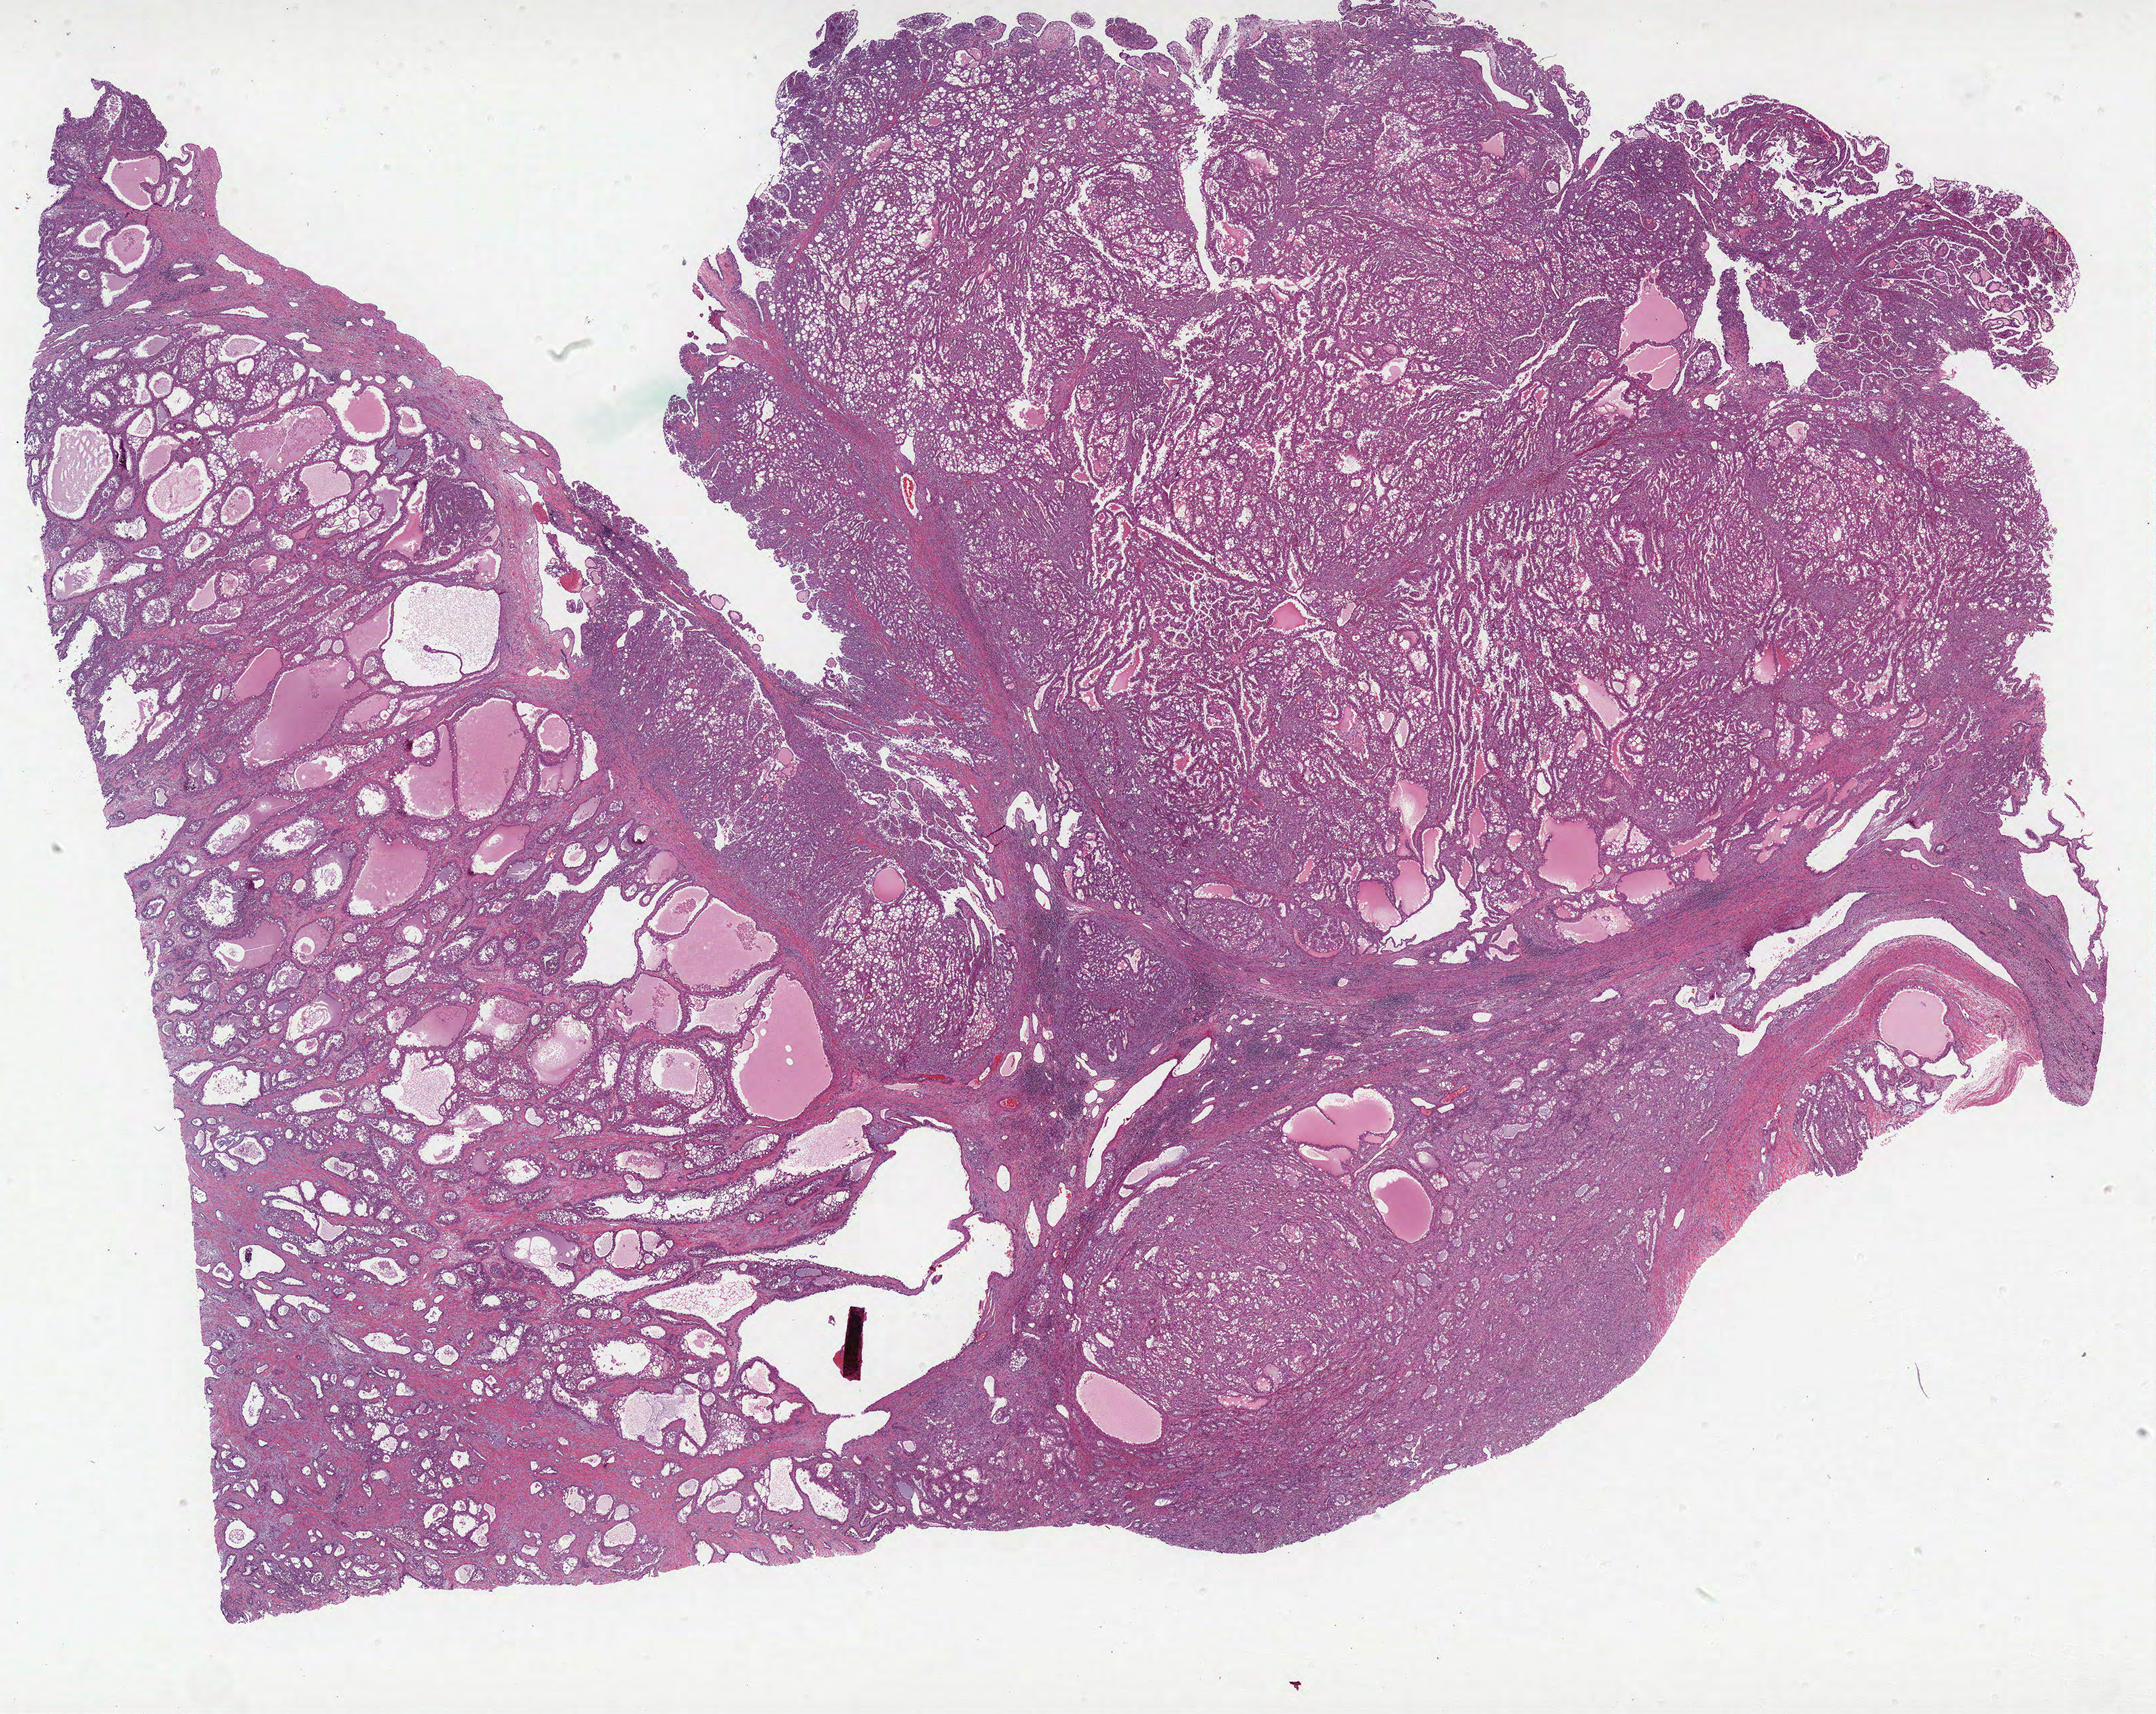
Whole-slide histology image, H&E — a low-resolution overview of the entire scanned area, about 25.7 x 20.4 mm; formalin-fixed paraffin-embedded (FFPE) diagnostic section; sample: primary tumour, kidney. Female patient; age at initial diagnosis 32 years.
Lymph nodes positive (case pathology): 3 of 26 examined. Histologic diagnosis: Papillary adenocarcinoma, NOS. AJCC pathologic stage: III. TNM: T3b N1 M0.